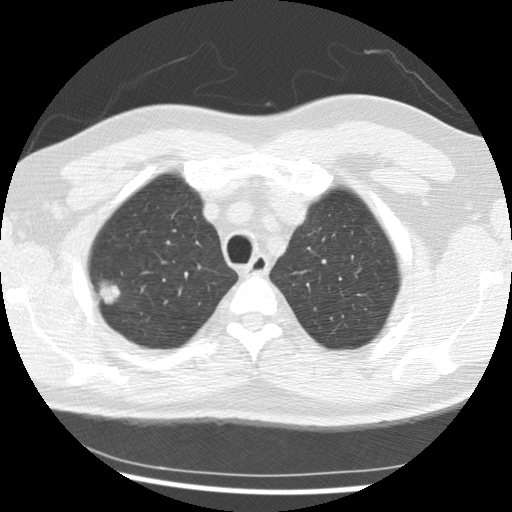
Axial slice from a low-dose chest CT screening exam. First (baseline) screen. Lung window (W 1500 / L -600 HU). 2.5 mm slice thickness. Standard (soft-tissue) reconstruction kernel (STANDARD). 120 kVp. Slice 49 of 265 in the series. 512 × 512 image matrix, field of view 340 × 340 mm. Male participant, aged 56 years at enrolment.
- Expert reader's lesion annotation, bounding box <84,274,132,315> (left, top, right, bottom; pixels).
- Screening reader's record for this exam (one nodule recorded; not confirmed to be the boxed lesion): non-calcified nodule or mass ≥4 mm, right upper lobe, 19 × 15 mm, spiculated (stellate) margins, soft tissue attenuation.
- Official screen result: positive, change unspecified: nodule(s) >= 4 mm or enlarging nodule(s), mass(es), or other non-specific abnormalities suspicious for lung cancer.
- Later outcome: lung cancer diagnosed 291 days after this screen — non-small cell carcinoma, right upper lobe, poorly differentiated (G3), stage IIIB (AJCC 6th edition), 20 mm at pathology.